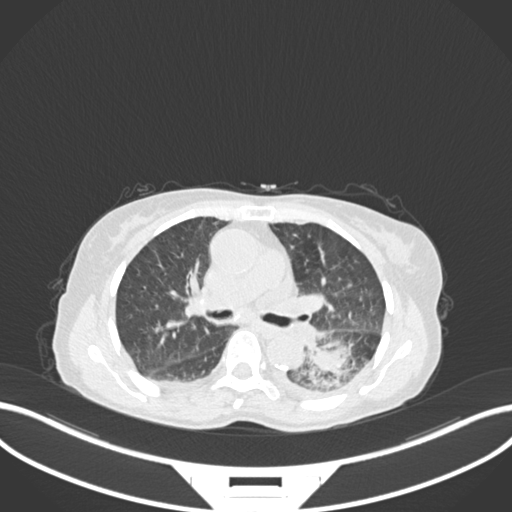
Chest CT, one axial slice. Slice 105 of 233 in the series (ordered by position). Reconstruction kernel B30f. Lung window (W 1500 / L -600 HU). 1 mm slice thickness. 512 × 512 image matrix, field of view 400 × 400 mm. Patient: female, 78 years. From the clinical record (not read from this slice): clinical TNM (as recorded): T3 N0 M1.
Structures marked on this image (bounding box drawn by a radiologist):
- lung tumour (recorded histology: squamous cell carcinoma): bounding box <296,326,371,392> (left, top, right, bottom; pixels)